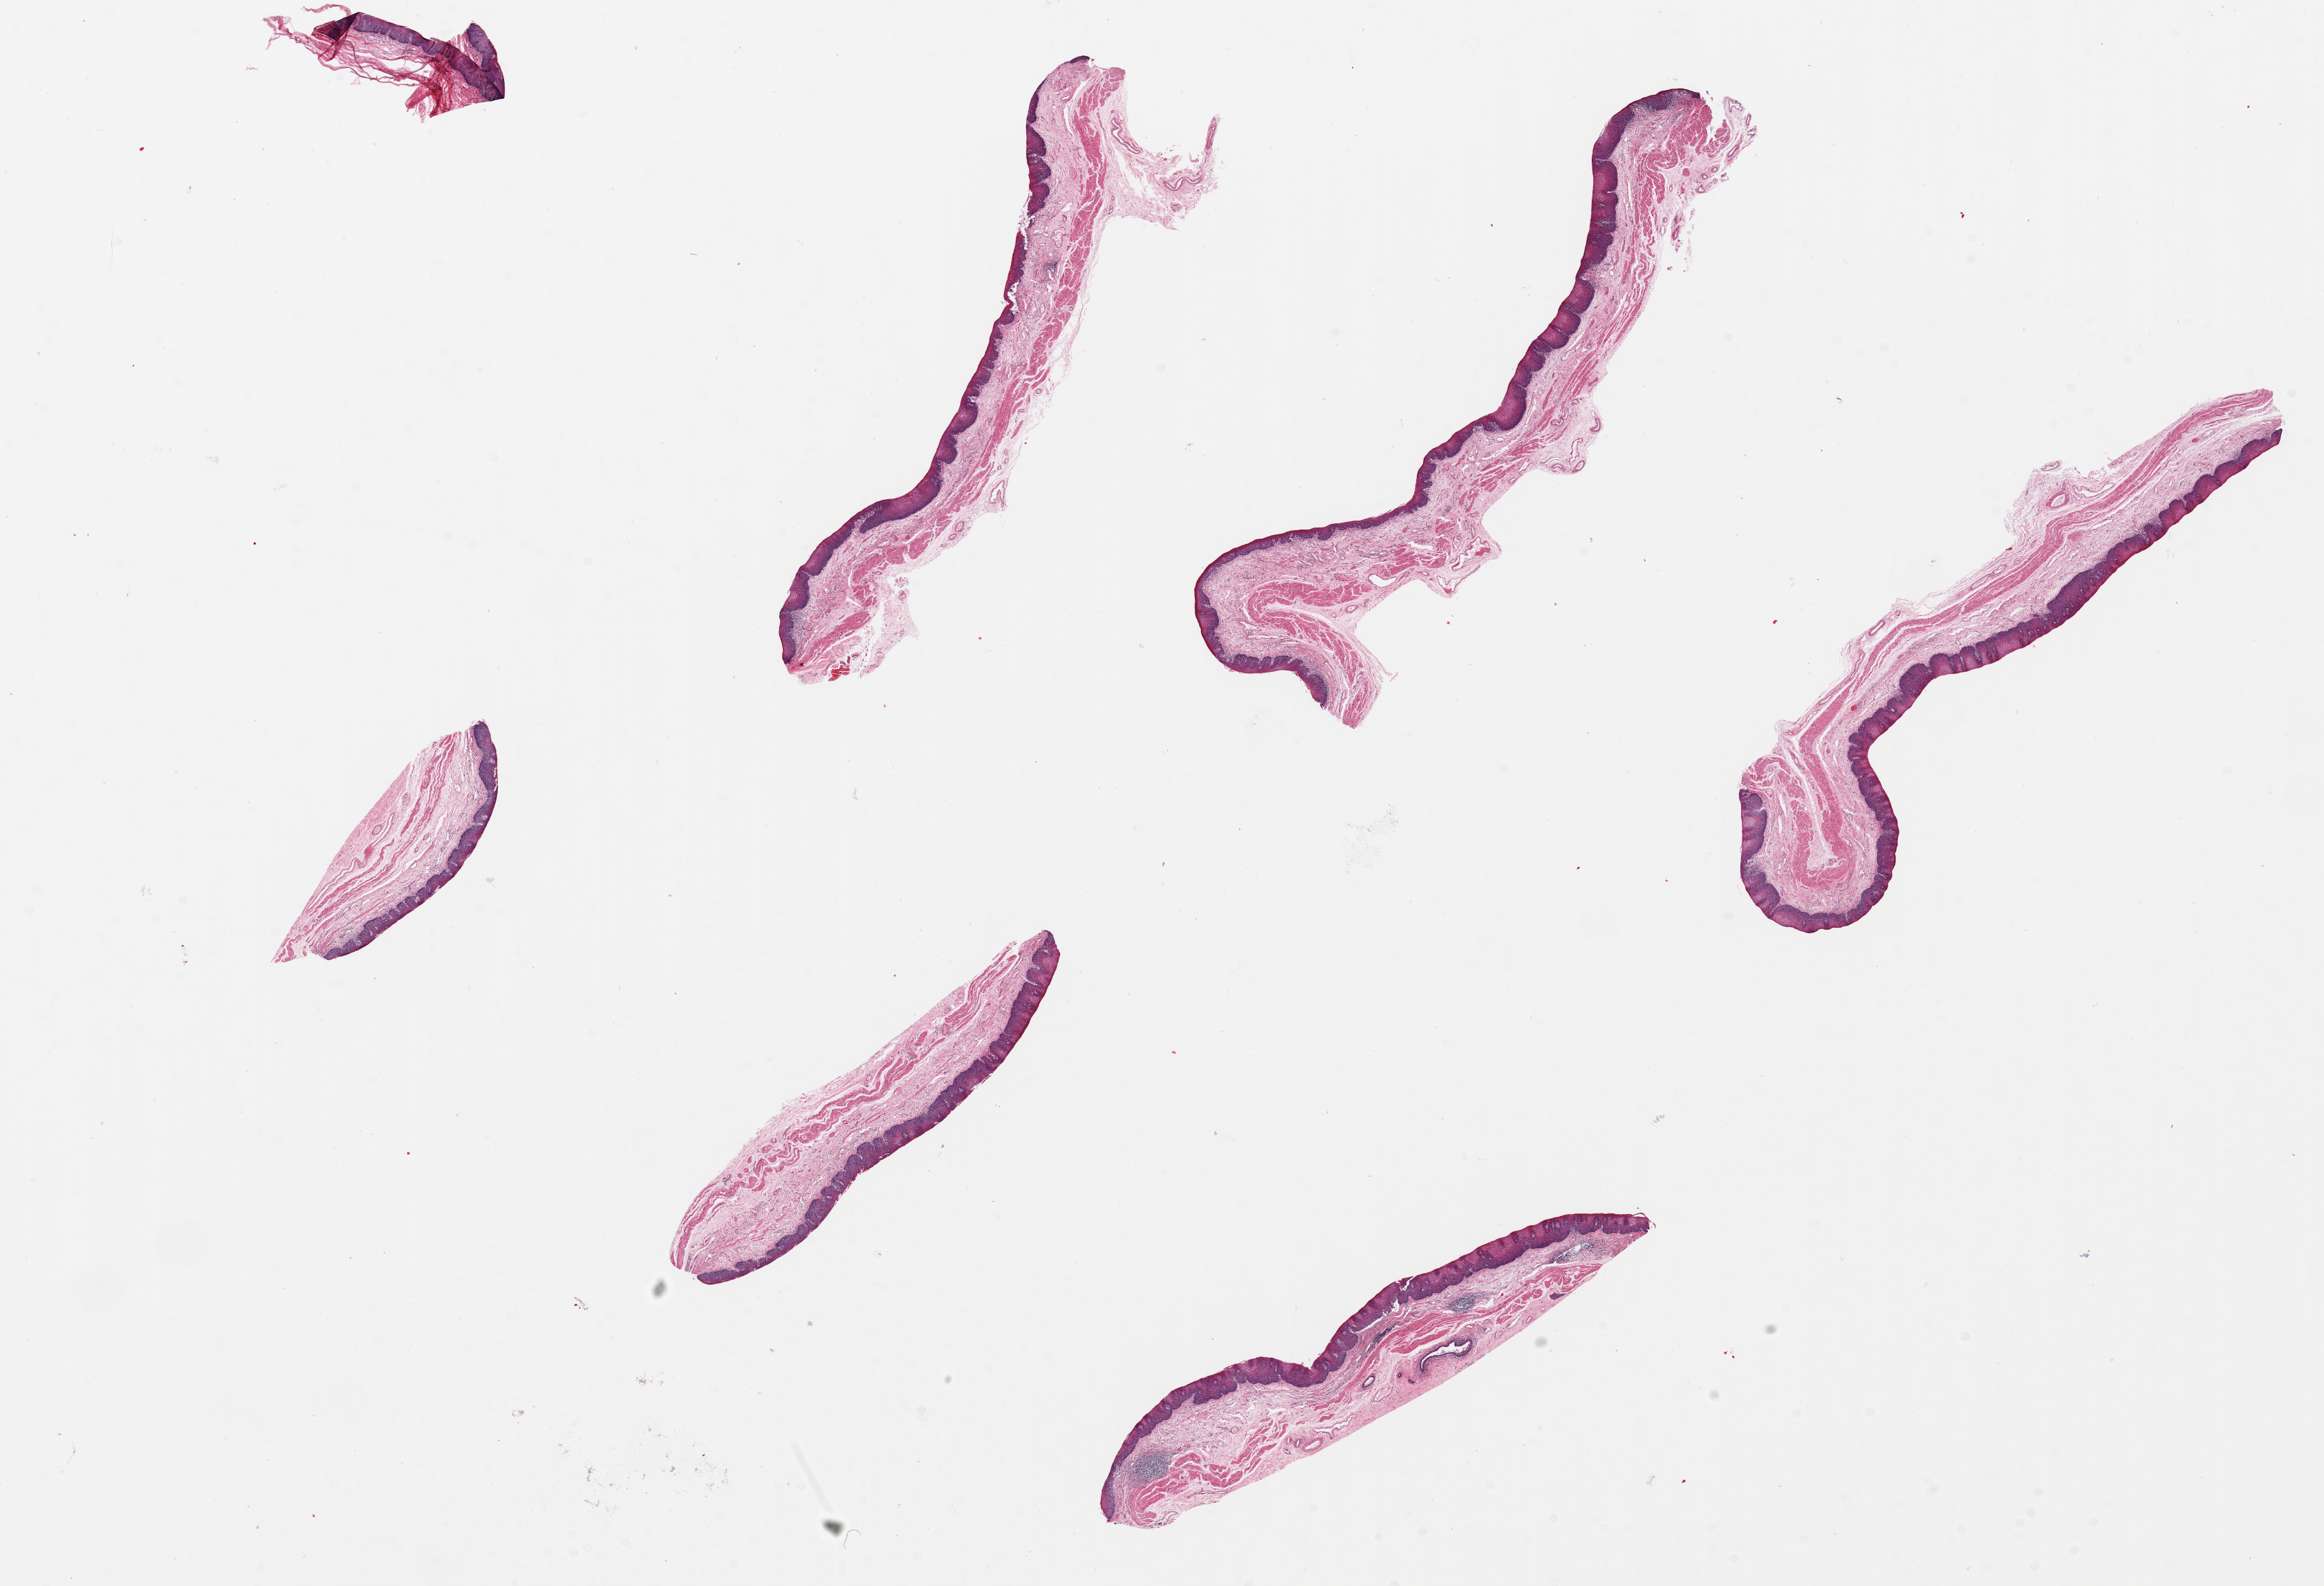
H&E whole-slide image, brightfield, a low-resolution overview of the entire scanned area, about 26.6 x 18.1 mm (from a 20x scan). PAXgene-fixed, paraffin-embedded tissue. Section of esophageal mucous membrane (target tissue). Donor tissue sample. Donor: female.
Review note (as recorded): 6 pieces, up to 9x2mm; mild chronic inflammation, good squamous mucosa.